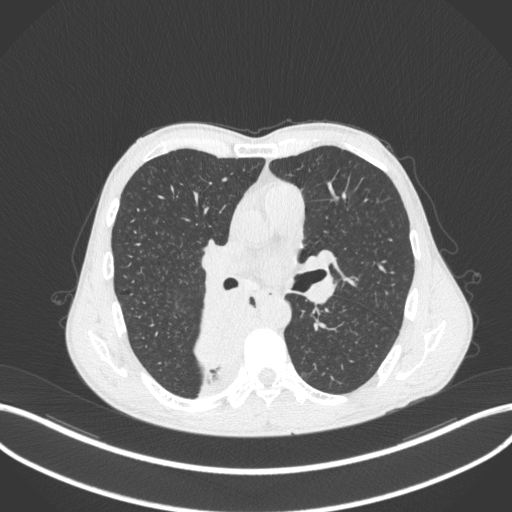
Chest CT, one axial slice; lung window (W 1500 / L -600 HU); 1 mm slice thickness; 512 × 512 image matrix. Patient: male, 58 years. From the clinical record (not read from this slice): clinical TNM (as recorded): T3 N1 M1.
Structures marked on this image (rectangle marked by the reading radiologist):
- lung tumour (recorded histology: squamous cell carcinoma): bounding box <191,290,253,372> (left, top, right, bottom; pixels)